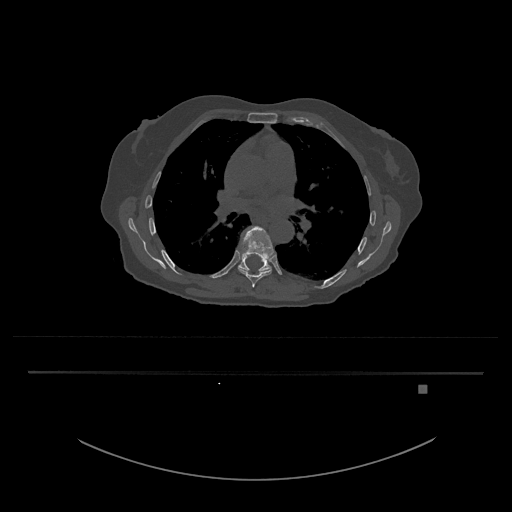
CT including the spine, one axial slice; position 788 of 797 along the scan axis; reconstruction kernel Br40s/3; 120 kVp; bone window (W 1800 / L 400 HU); 0.5 mm slice thickness; 512 × 512 image matrix, field of view 500 × 500 mm. Female patient, age 57 years. Case-level facts recorded for this patient, not image findings: primary cancer: cervical.
Structures marked on this image (semi-automatically segmented with operator editing):
- T8 vertebra: box from (x=238, y=226) to (x=274, y=288) px
- T9 vertebra: (x=237, y=250)–(x=272, y=272)